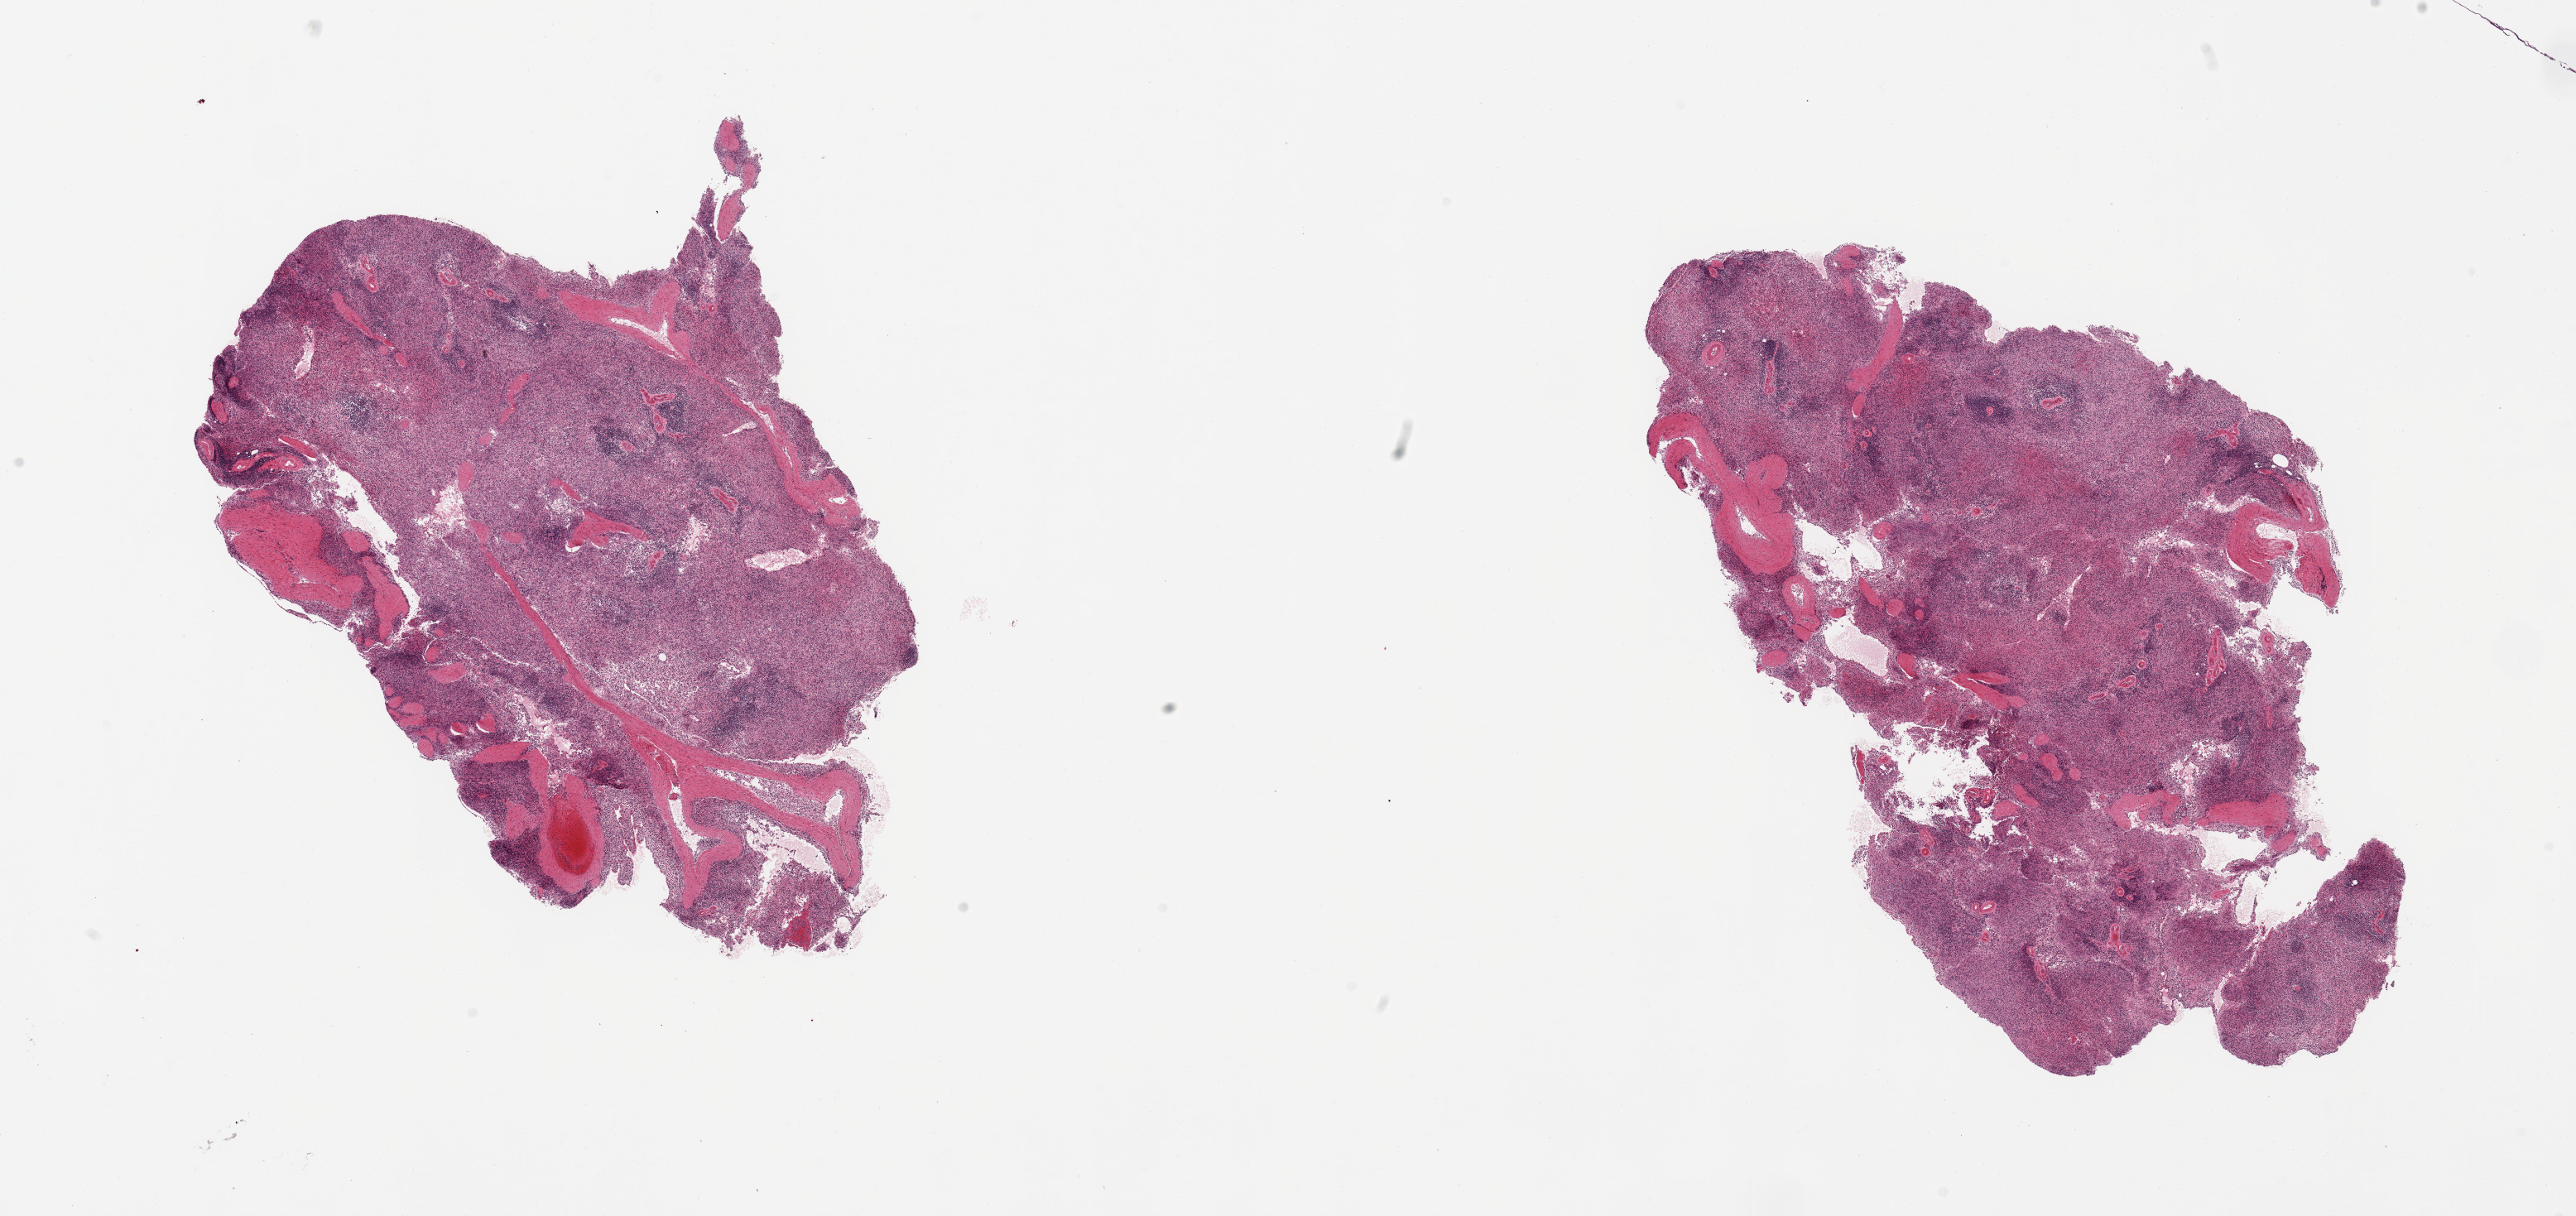
Hematoxylin and eosin (H&E) whole-slide image, brightfield — shown as a low-resolution overview of the whole scanned area (about 24.6 x 11.6 mm, from a 20x scan). PAXgene-fixed paraffin-embedded (PFPE) section. Target tissue: spleen. Tissue donor sample. Male donor.
* reviewer comment on this tissue sample: 2 pieces, moderate-marked congestion